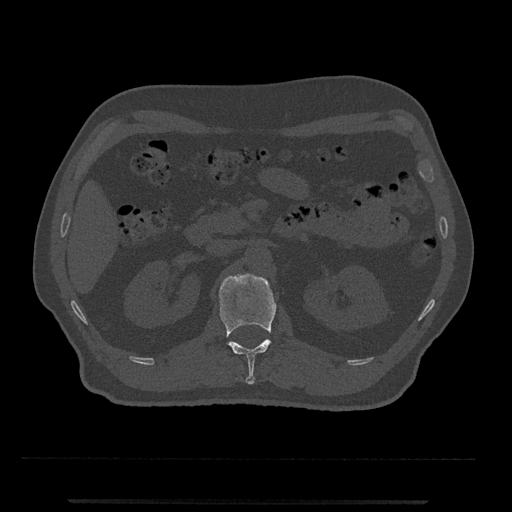
CT including the spine, one axial slice; position 326 of 797 along the scan axis; reconstruction kernel Br40s/3; 120 kVp; bone window (W 1800 / L 400 HU); 0.5 mm slice thickness; 512 × 512 image matrix, field of view 419 × 419 mm. Male patient, age 63 years. Case-level facts recorded for this patient, not image findings: primary cancer: prostate.
Structures marked on this image (semi-automatically segmented with operator editing):
- L1 vertebra: bounding box [x1, y1, x2, y2] px = [219, 274, 277, 385]